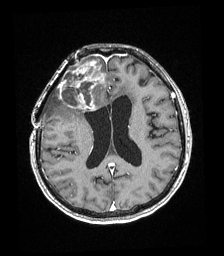
Brain MRI from a brain-tumour surgery series, one axial slice; slice 86 of 192 in the series (ordered by position); T1-weighted post-contrast; 1 mm slice thickness; 224 × 256 image matrix. Case-level facts recorded for this patient, not image findings: histopathology: Astrocytoma; WHO grade: 4.
Outlined on this slice (expert manual segmentation):
- tumour: bounding box <59,61,105,109> (left, top, right, bottom; pixels)